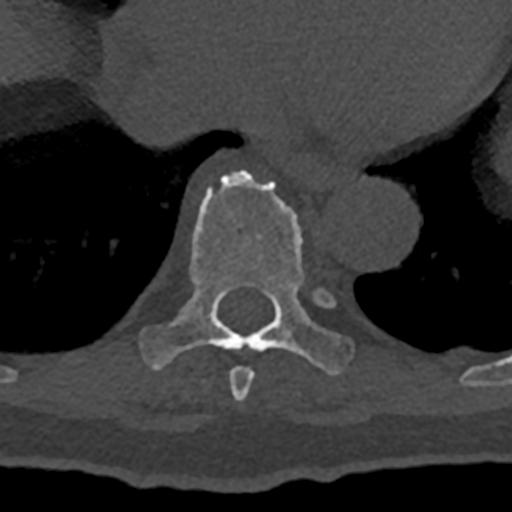
CT including the spine, one axial slice; bone window (W 1800 / L 400 HU); 512 × 512 image matrix, field of view 160 × 160 mm. Male patient, age 74 years. Case-level facts recorded for this patient, not image findings: primary cancer: renal; vertebrae with lytic lesions (as recorded): T10, L1, L2, L3, L4, L5.
Outlined on this slice (semi-automatically segmented with operator editing):
- T8 vertebra: box from (x=229, y=367) to (x=254, y=402) px
- T9 vertebra: (x=141, y=170)–(x=353, y=375)